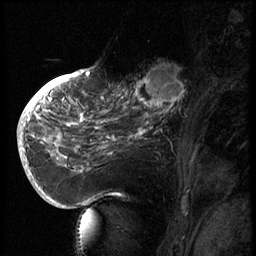
Breast MRI (dynamic contrast-enhanced), one sagittal slice; position 27 of 66 along the scan axis; 3 images stored at this slice position (order not interpretable as contrast timing); 1.5 T; TE 4.2 ms, TR 8.9 ms; 2.5 mm slice thickness; 256 × 256 image matrix, field of view 200 × 200 mm. Patient: female, 56 years. Case-level facts recorded for this patient, not image findings: setting: breast cancer imaged before/during neoadjuvant chemotherapy.
Outlined on this slice (semi-automatic segmentation, software-assisted and operator-edited):
- analysis volume of interest (the breast-tissue region the enhancement analysis was run in; not a lesion): bounding box <129,62,194,127> (left, top, right, bottom; pixels)
- tumour enhancement mask (voxels above the 140 % enhancement threshold inside the analysis volume of interest): <135,65,187,124>